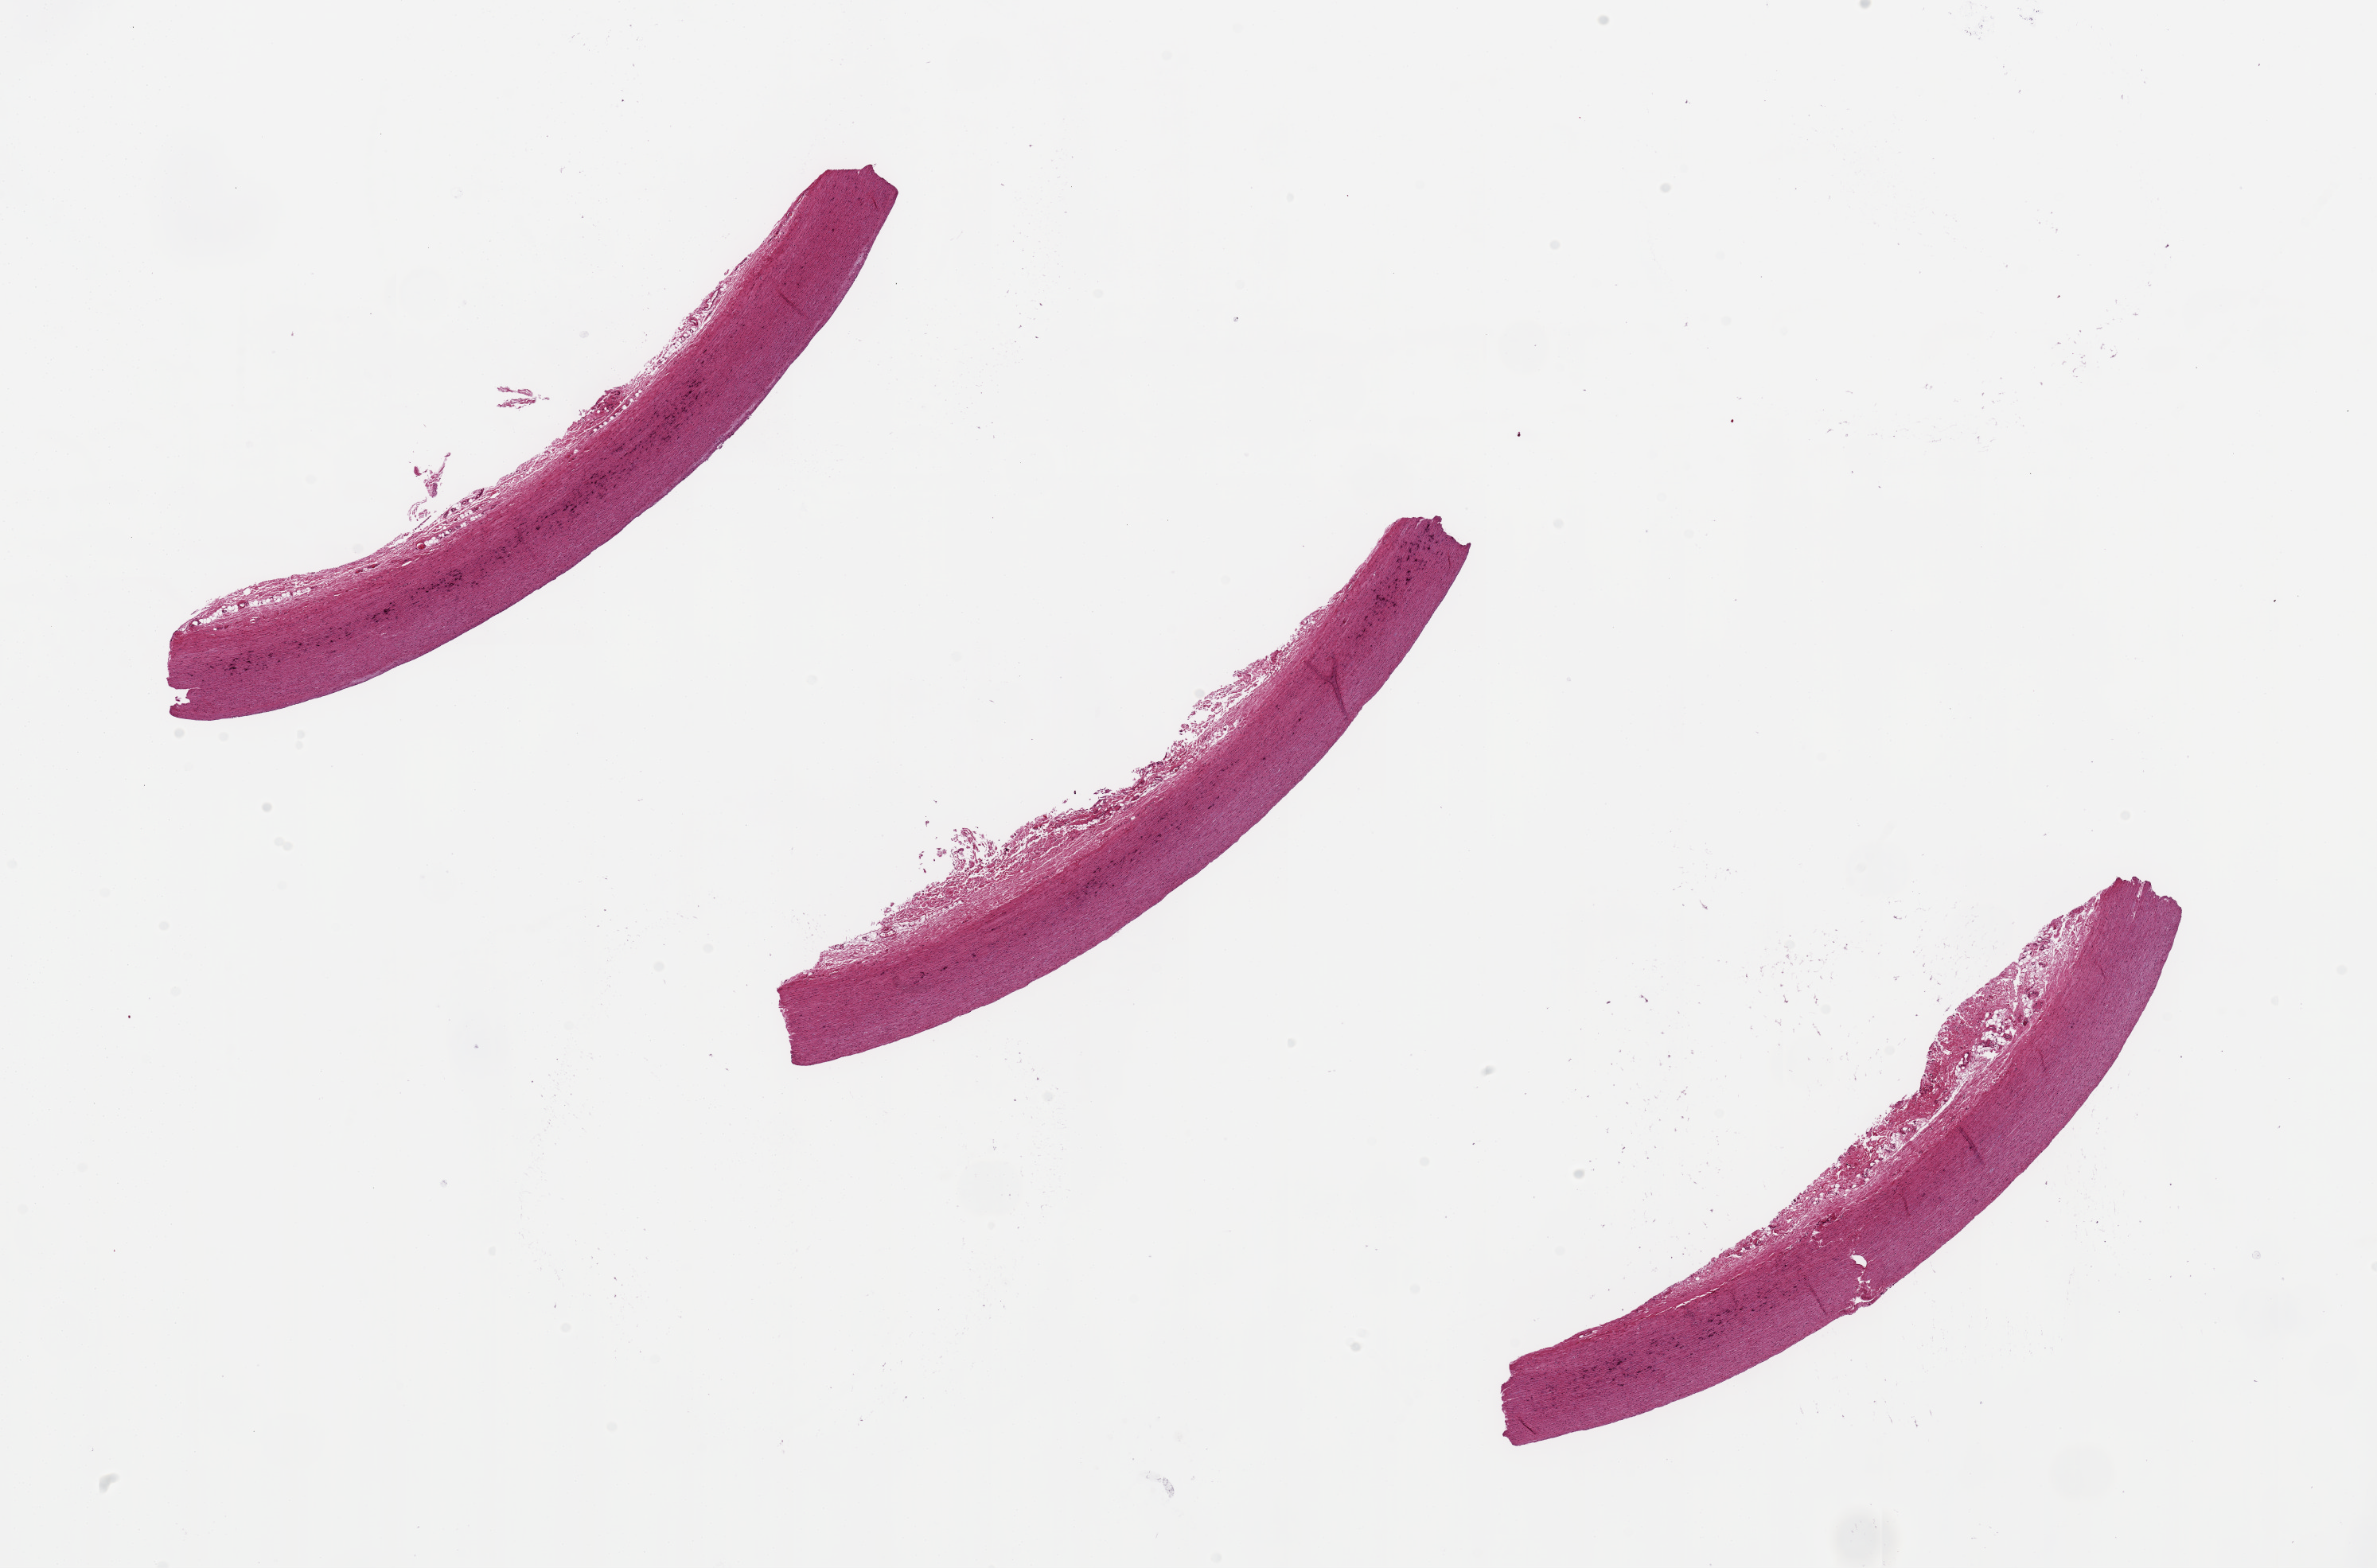
Digitized hematoxylin and eosin (H&E)-stained section, a low-resolution overview of the entire scanned area, about 23.6 x 15.6 mm. PAXgene-fixed paraffin-embedded (PFPE) section. Sampled site (target tissue): aorta. Donor tissue sample. Donor: male.
- reviewer comment on this tissue sample: 3 ~8x1 mm pieces